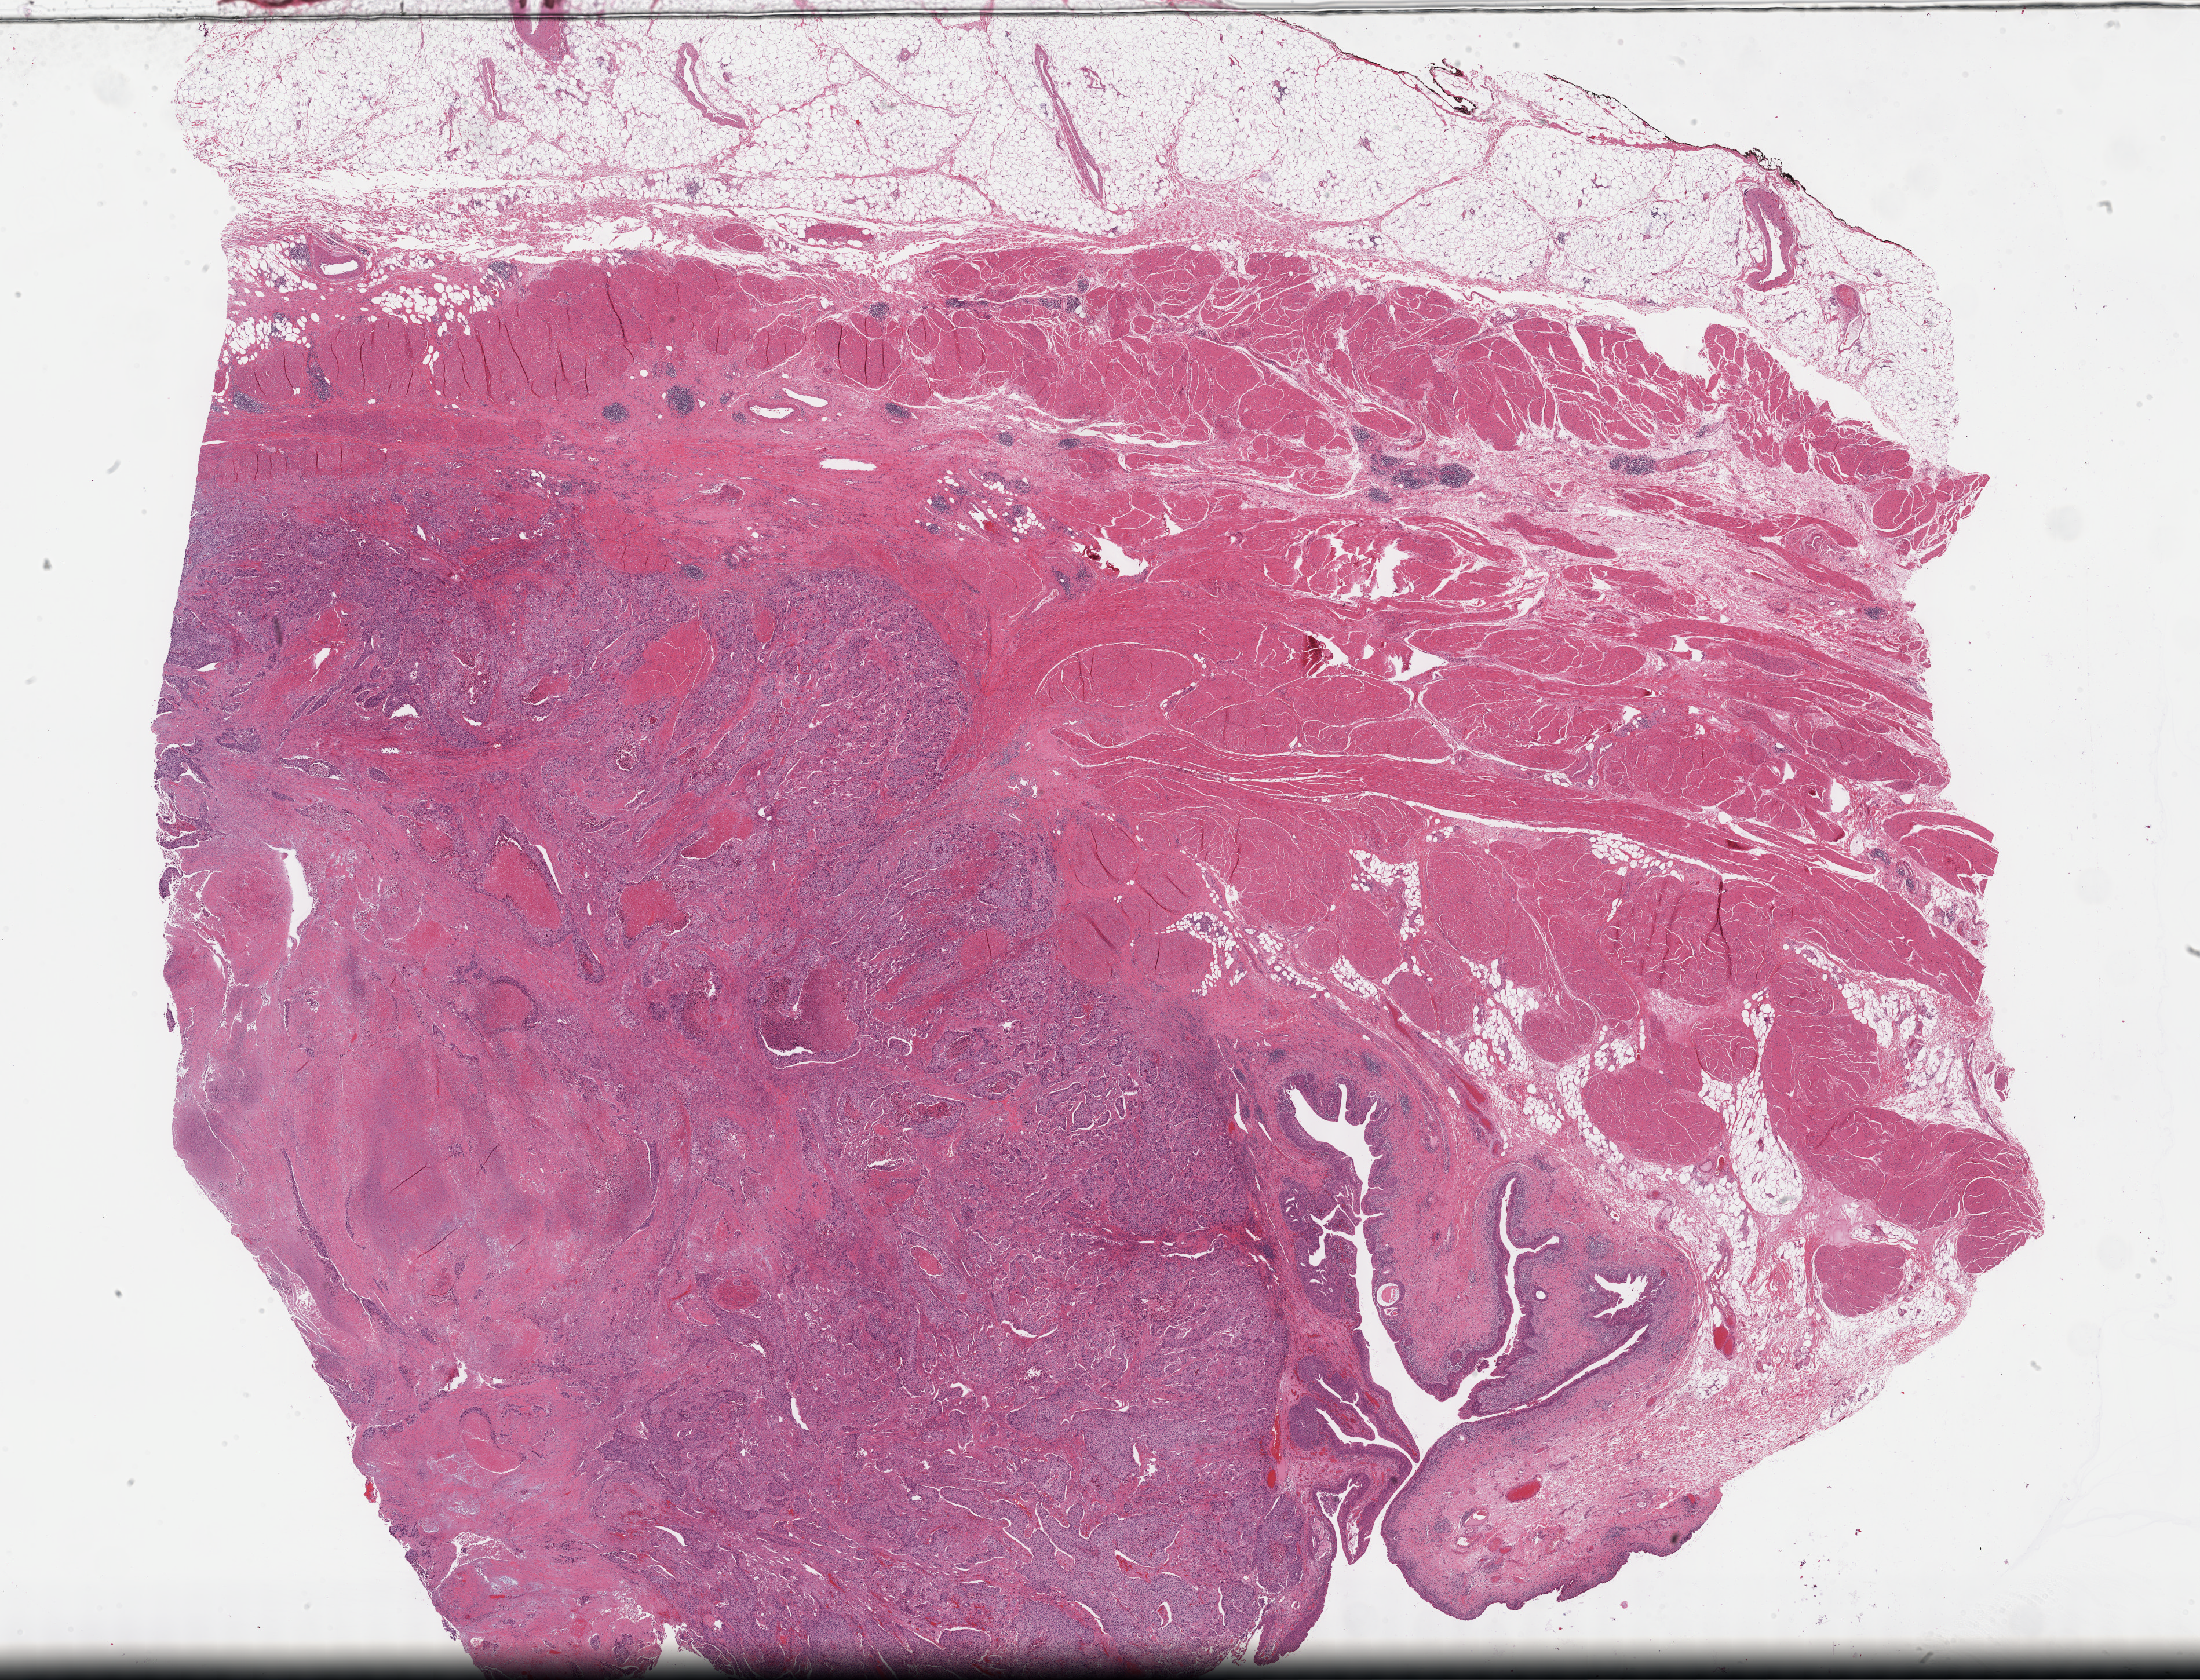
H&E whole-slide image — low-resolution overview of the scanned area, about 30.7 x 23.5 mm (from a 40x scan). FFPE section. Bladder, primary tumour sample. Patient: male, age at initial diagnosis 76 years. Histologic grade: high grade.
AJCC pathologic stage: III (7th edition). Lymph nodes positive (case pathology): 0 of 33 examined. Pathologic diagnosis: Transitional cell carcinoma.